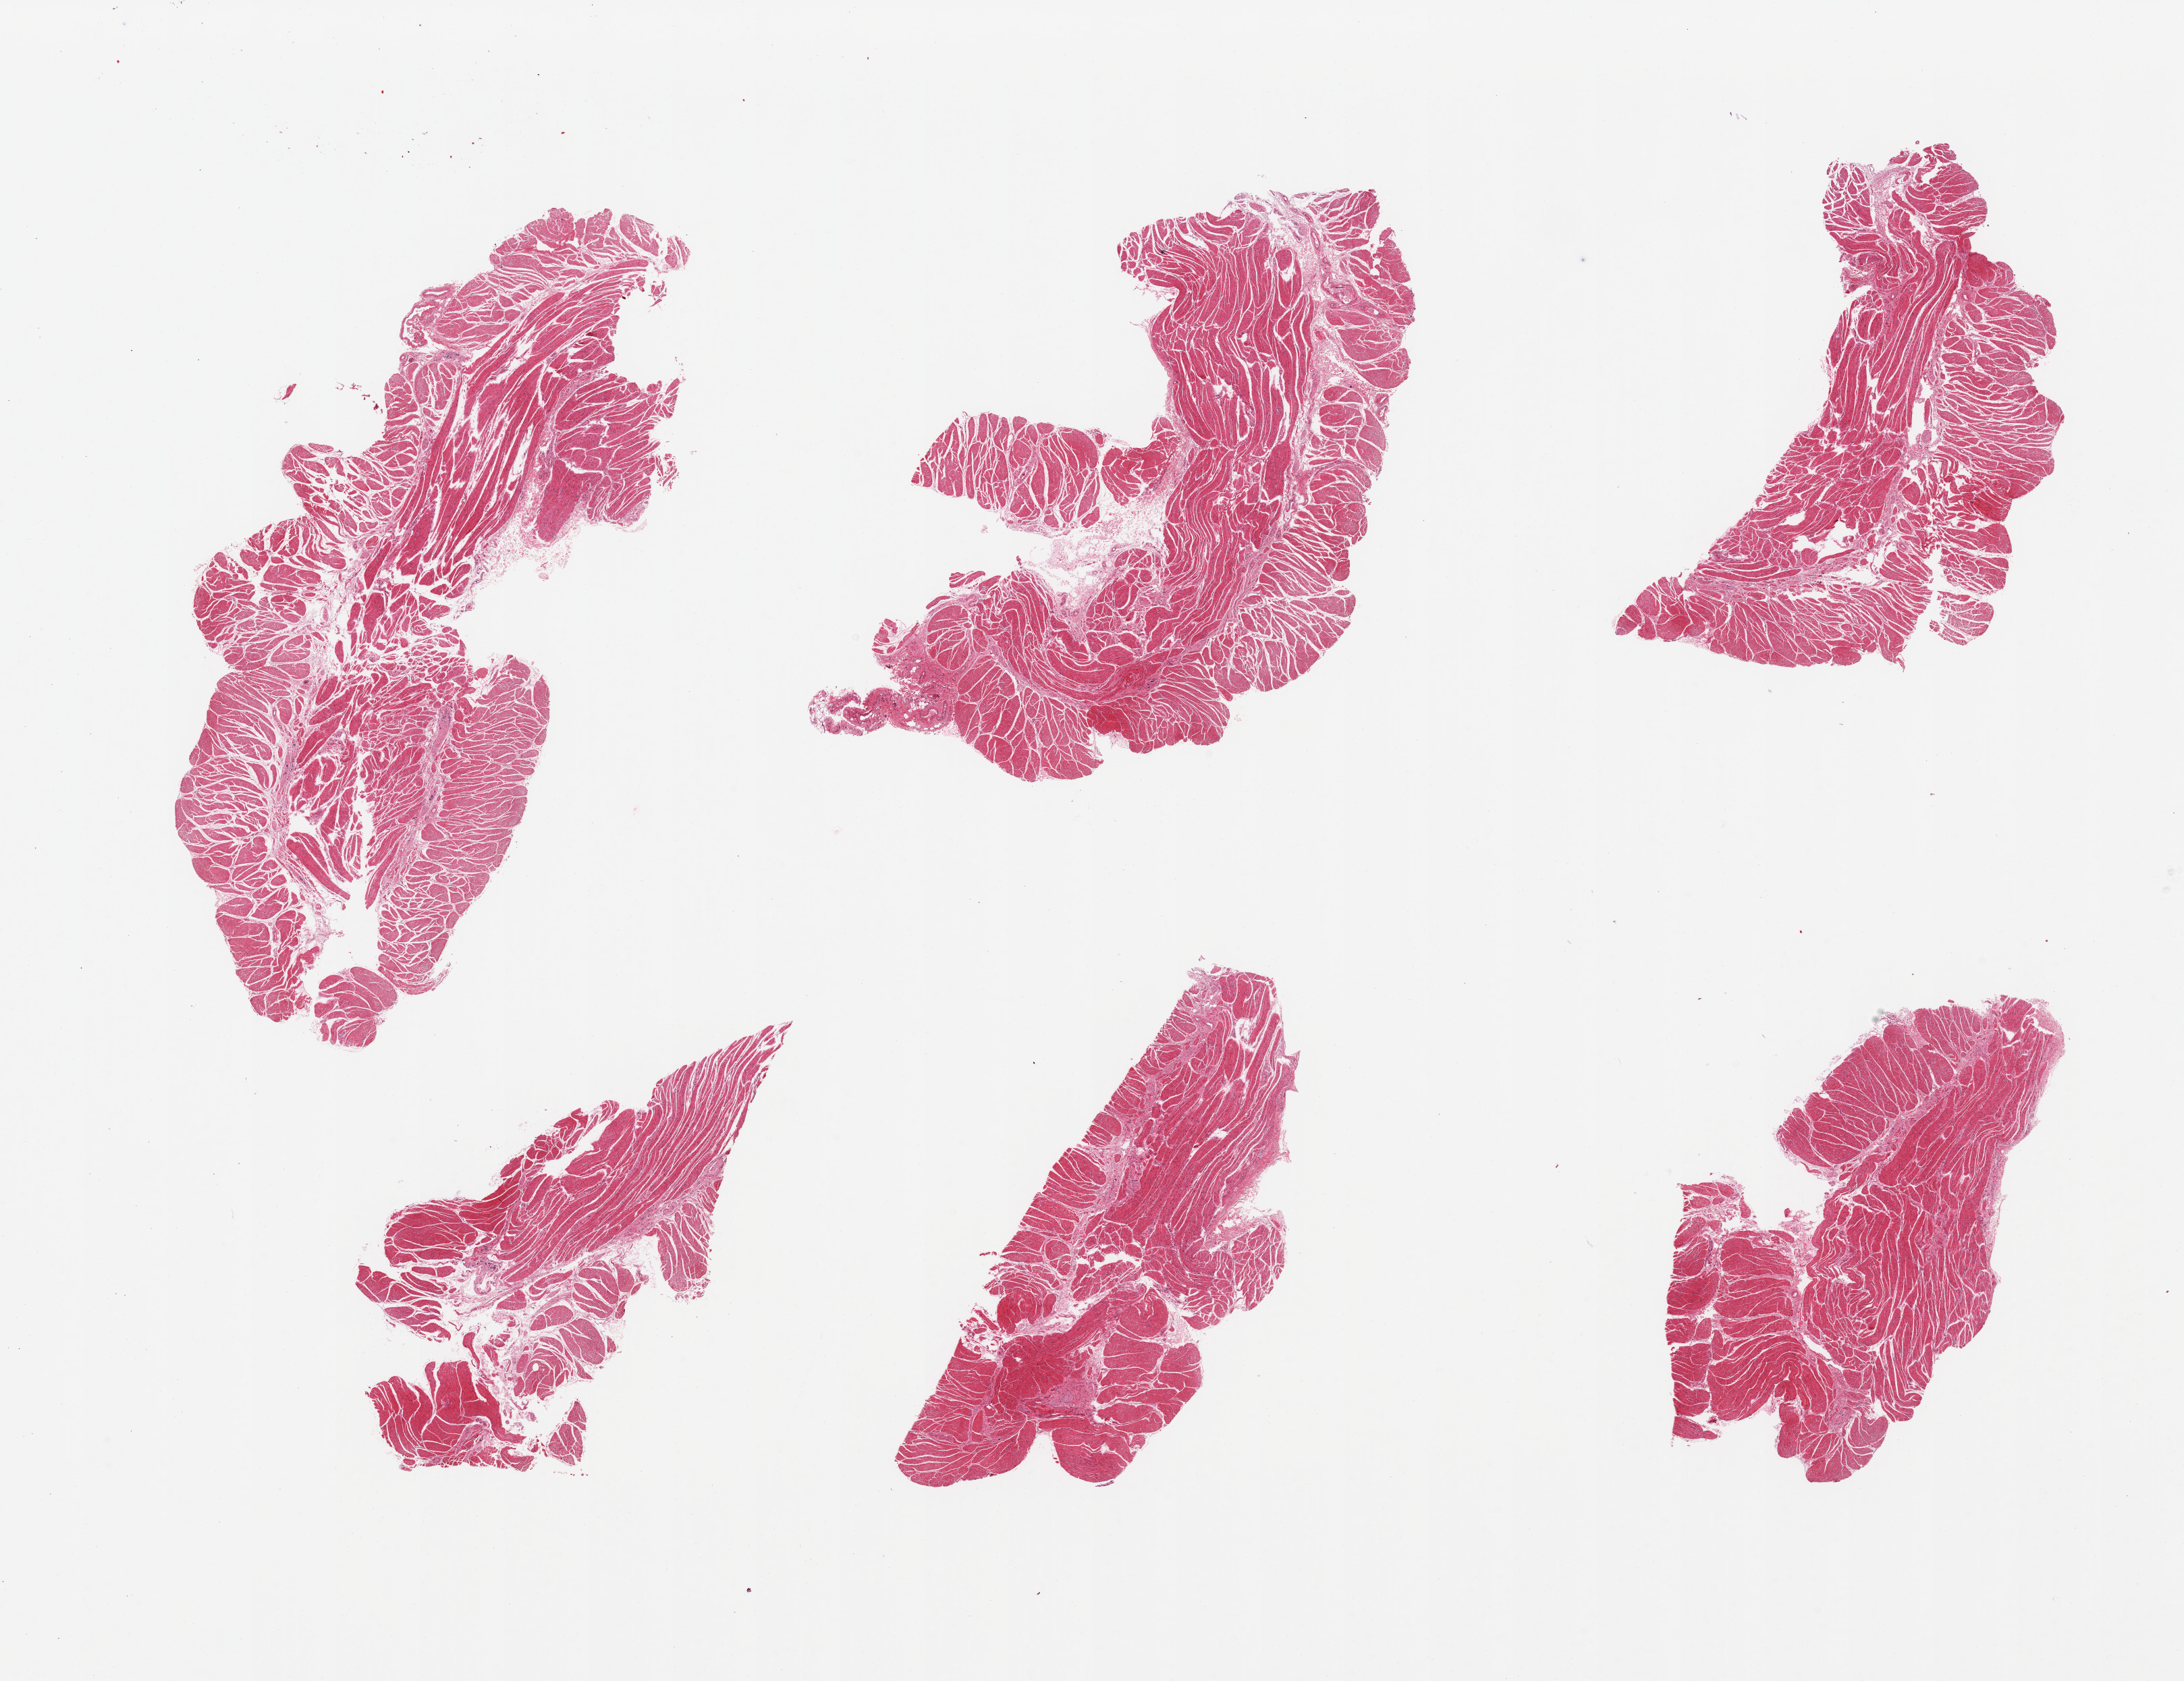
Digitized hematoxylin and eosin (H&E)-stained section — whole scanned area (about 25.6 x 19.7 mm, acquisition: 20x scan) shown as a low-resolution overview, PAXgene-fixed paraffin-embedded (PFPE) section, section of esophageal muscle (target tissue), tissue donor sample. Donor sex: male.
• pathologist's review note for this sample: 6 pieces, confirmed target muscularis